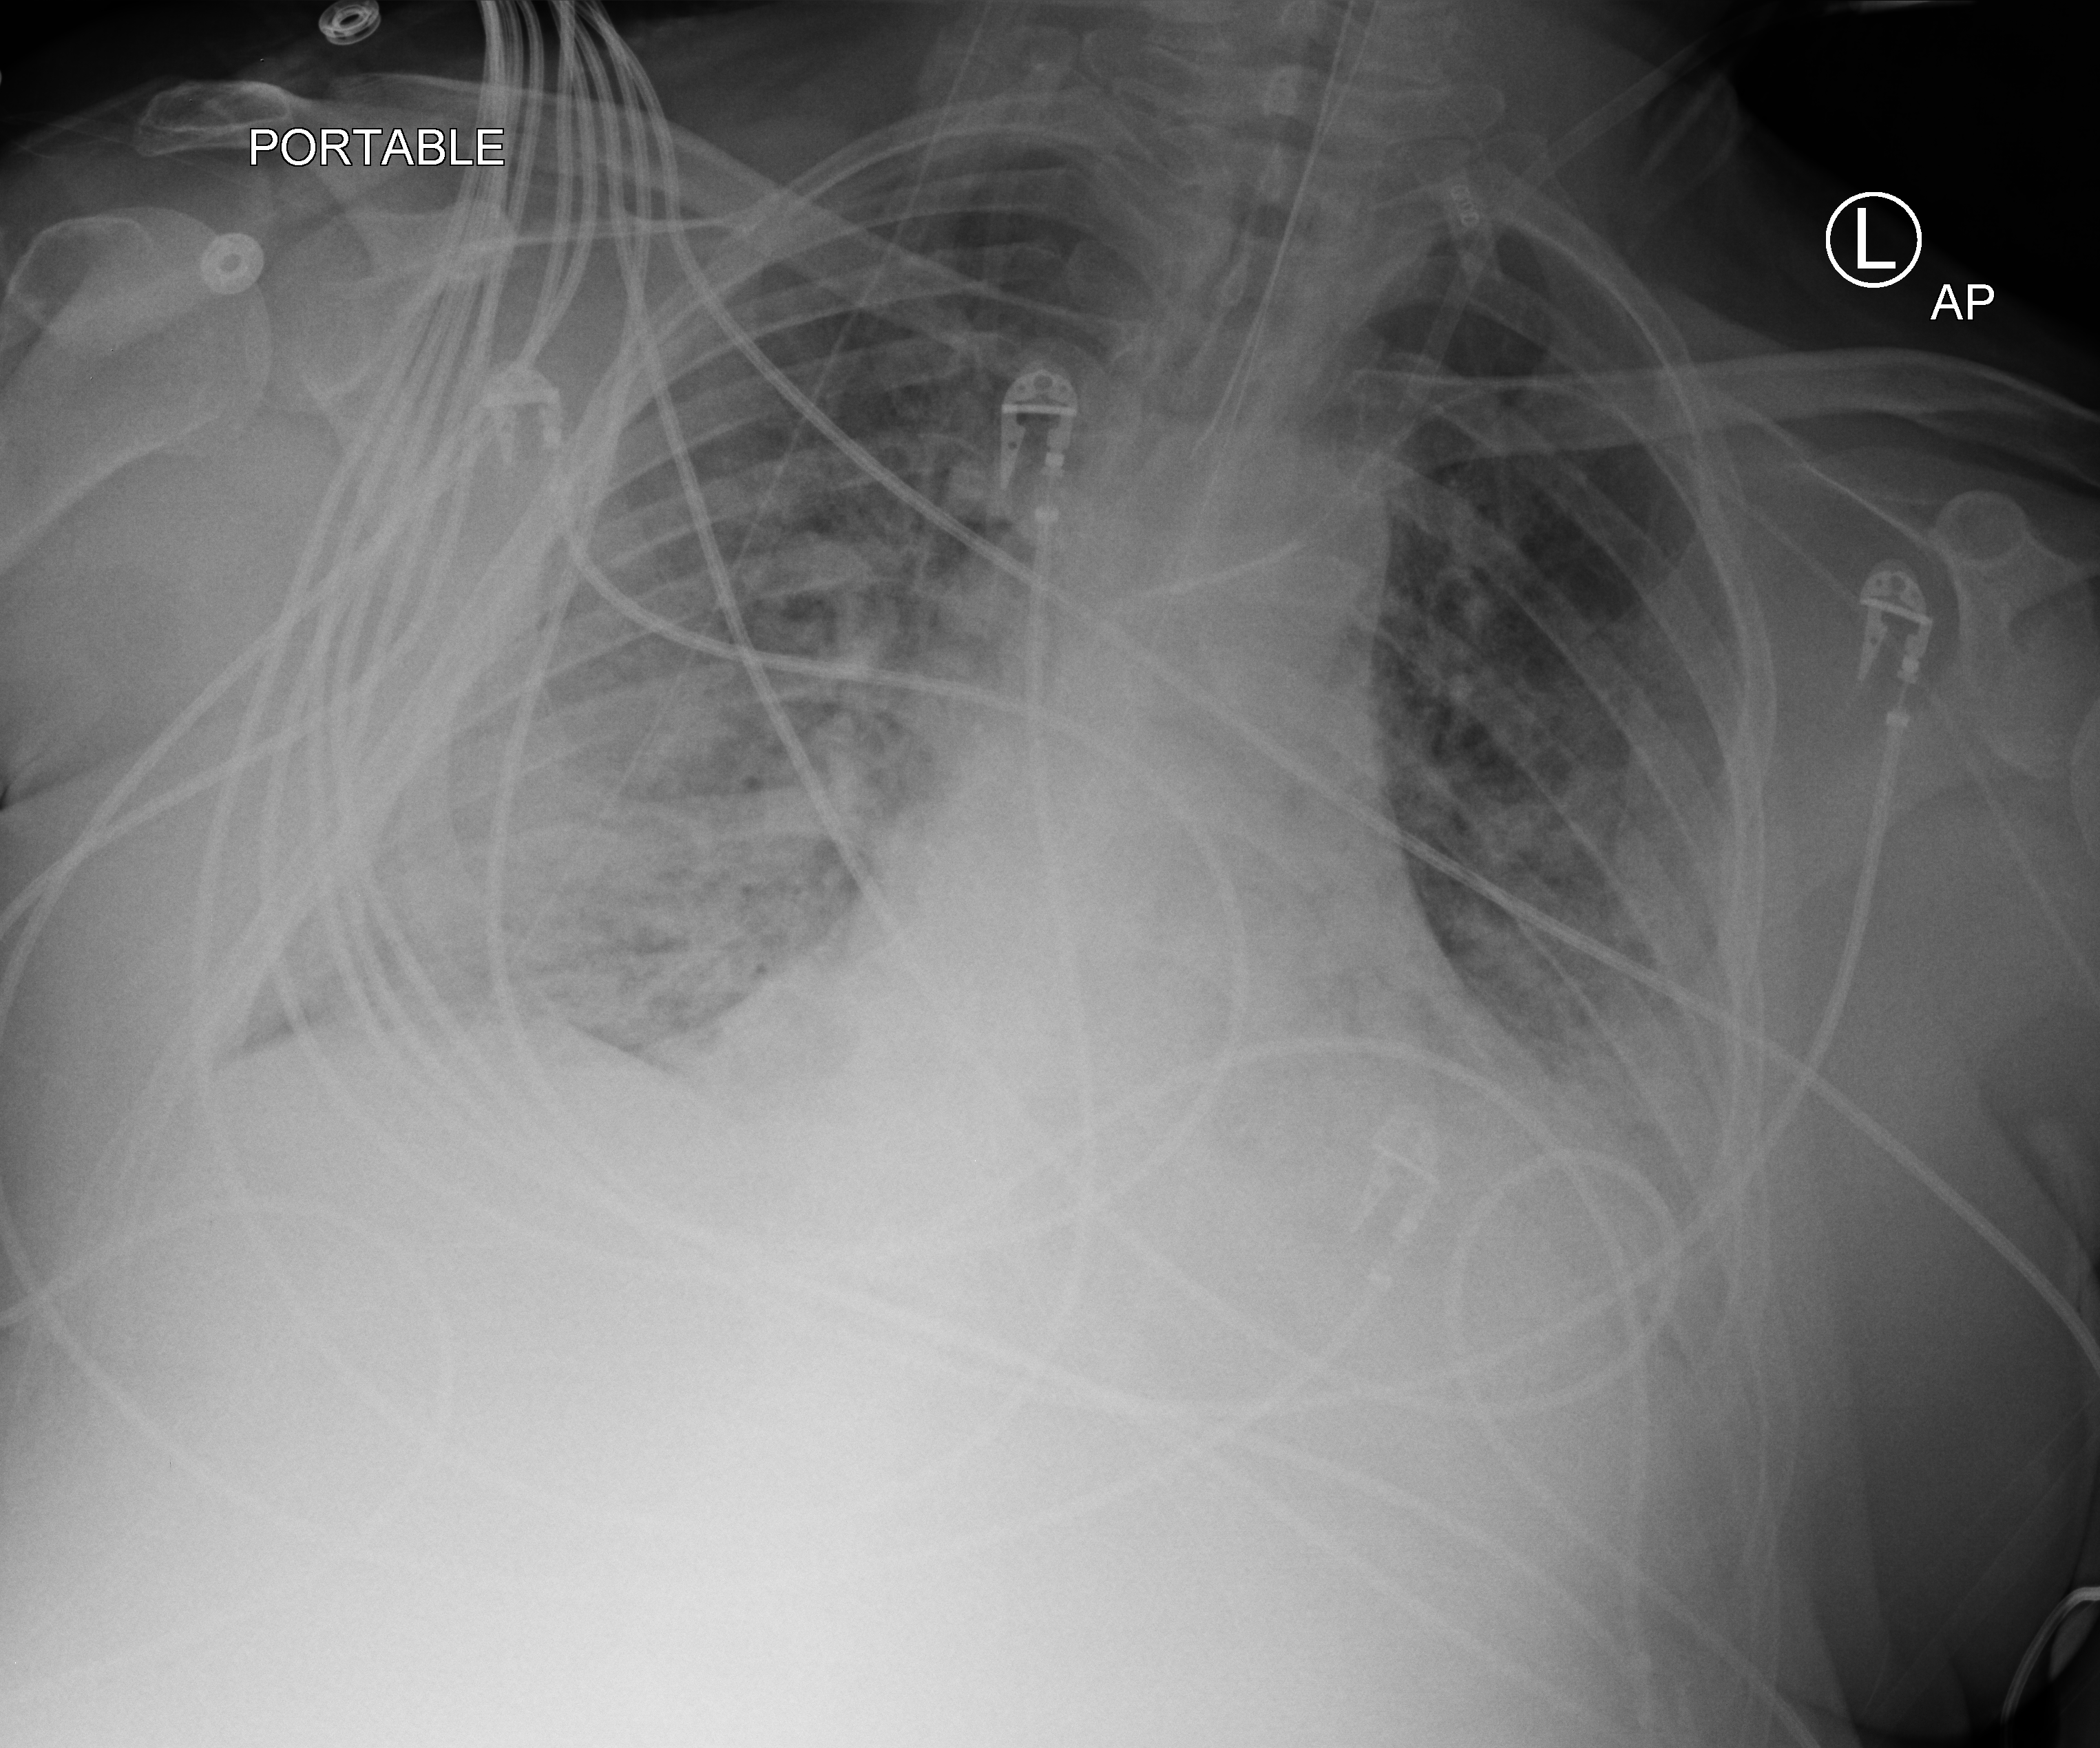
Bedside chest radiograph (computed radiography); anteroposterior (AP) projection. Patient hospitalised with COVID-19; male, aged 18–59 years.
From the hospital-stay record, not from the radiograph (when in the stay this image was taken is not recorded): mechanically ventilated during this hospital stay: yes; diabetes (admission record): no.